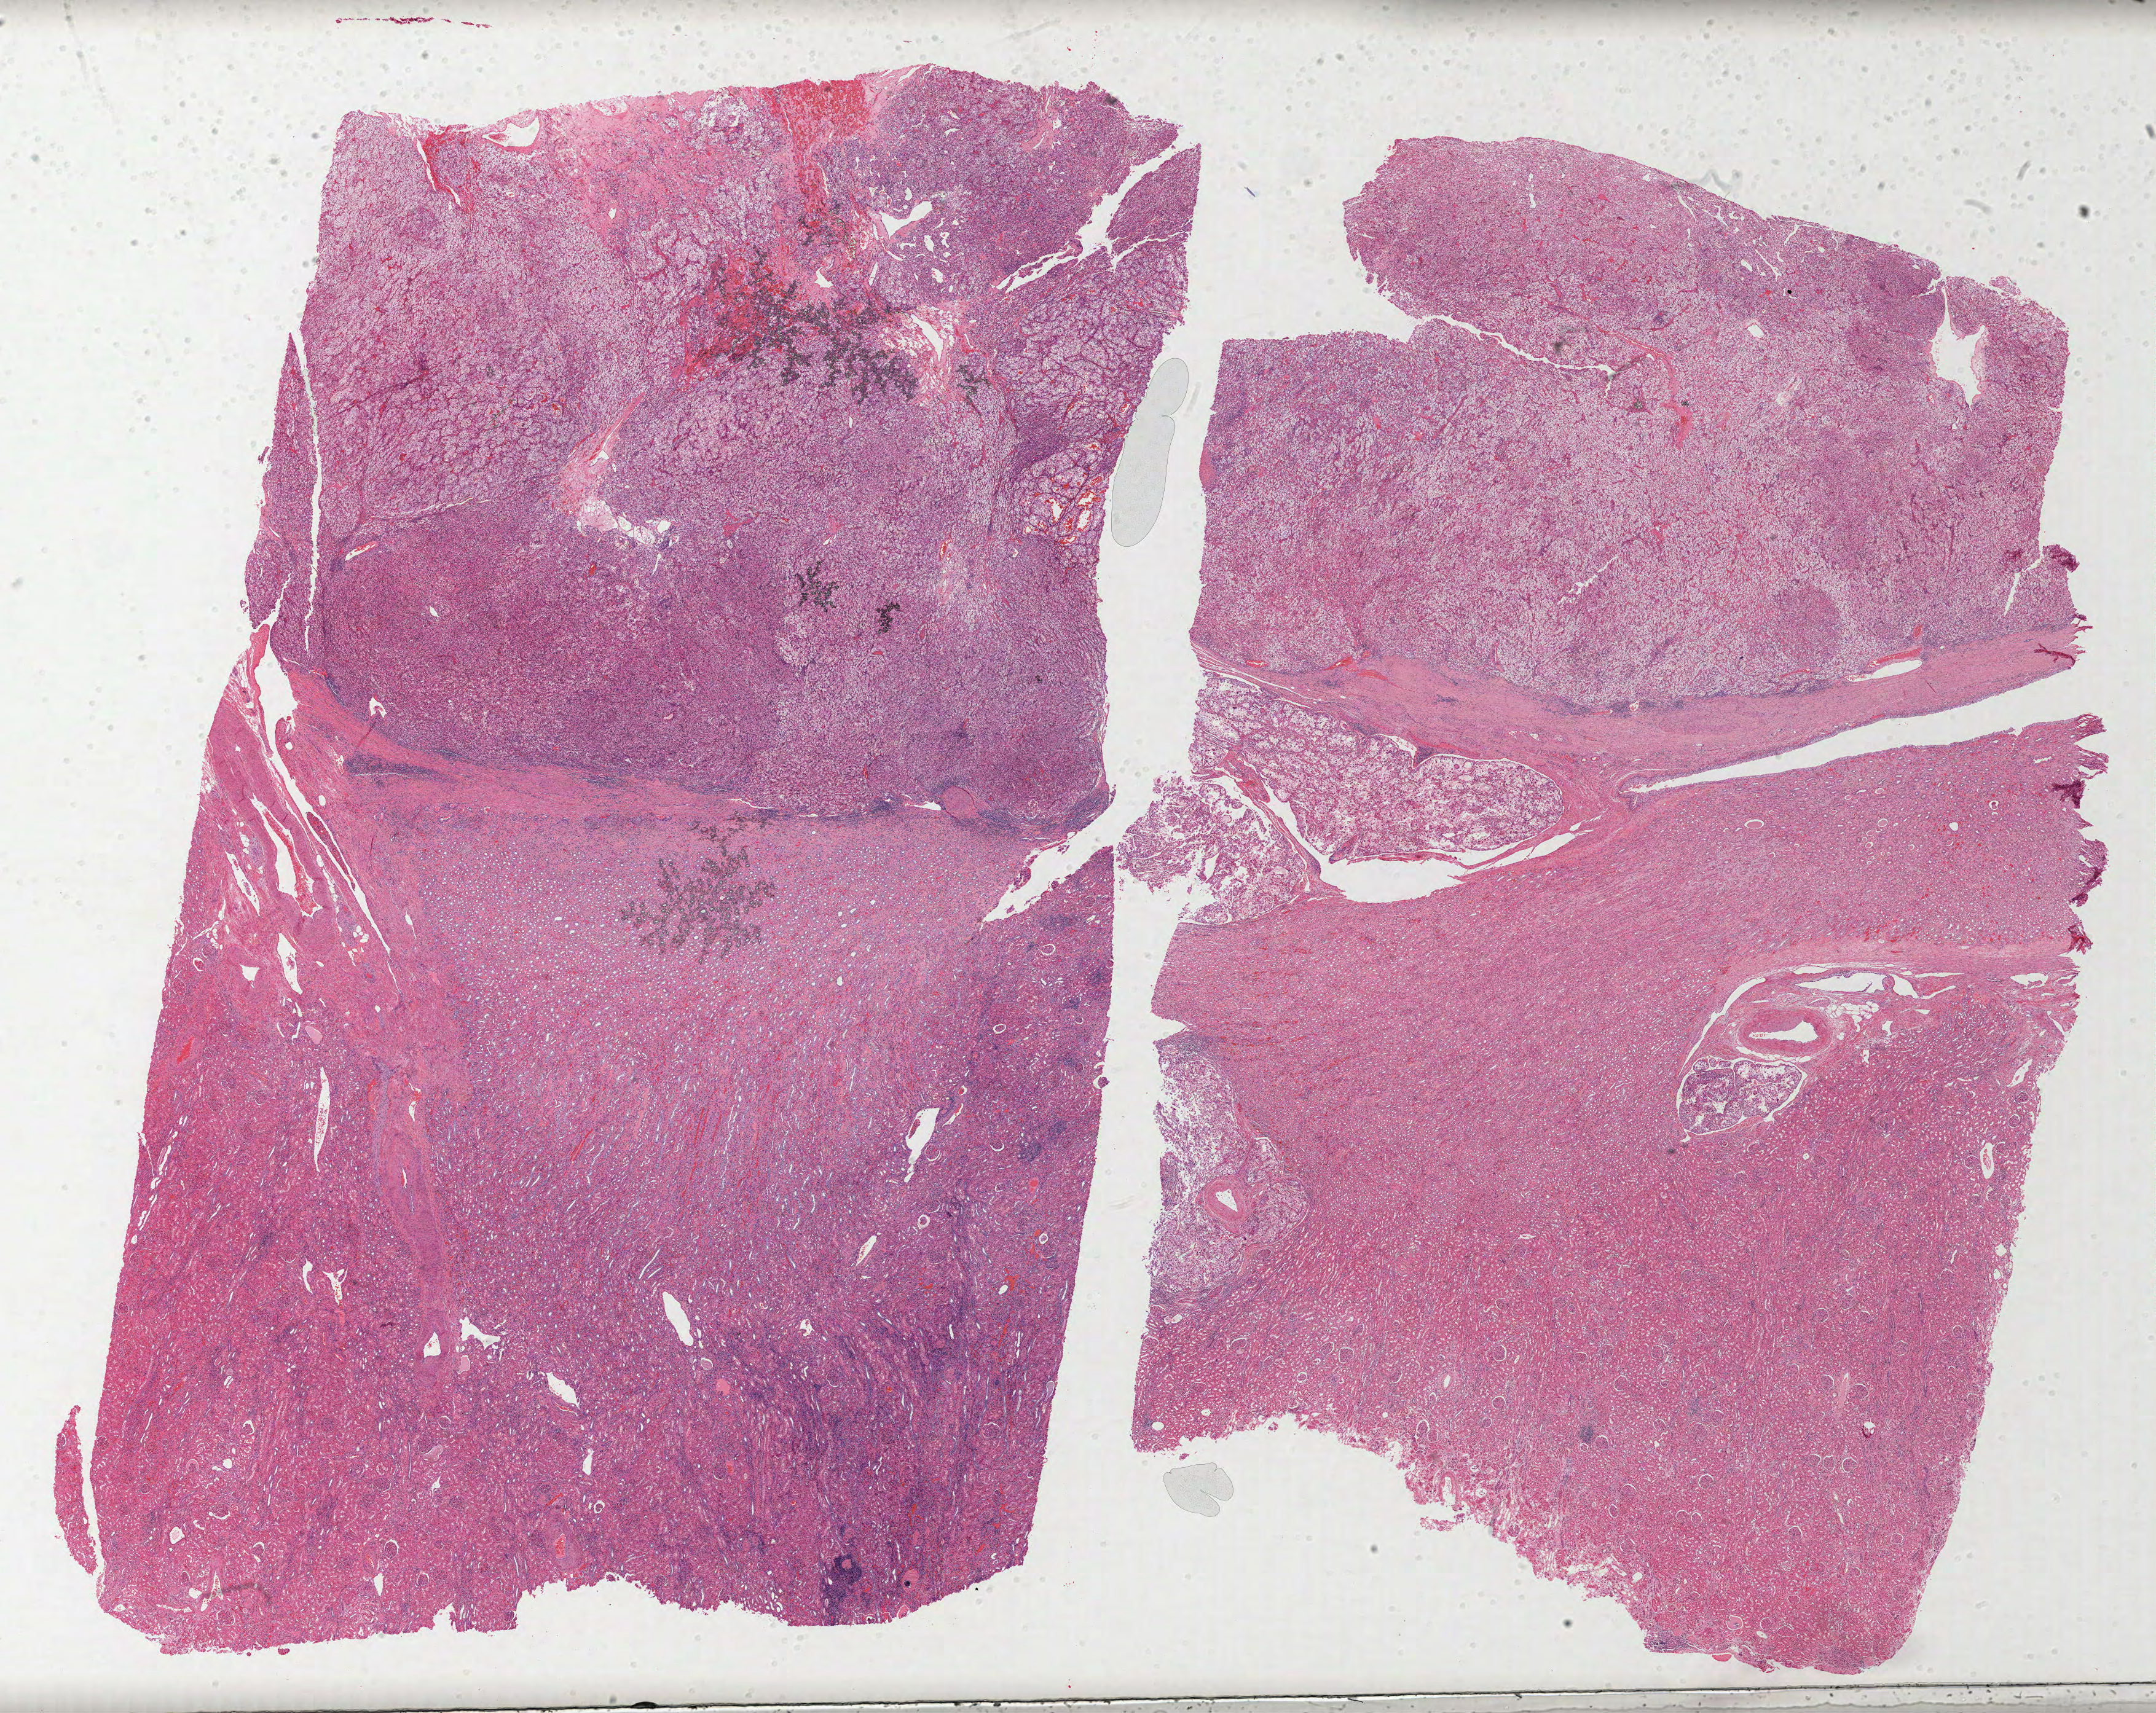
Digitized H&E-stained tissue section (whole slide) — a low-resolution overview of the entire scanned area, about 28.3 x 22.5 mm. Formalin-fixed paraffin-embedded (FFPE) diagnostic section. Sample: primary tumour, kidney. Male patient; age at initial diagnosis 55 years. Histologic grade: G2 (moderately differentiated).
• diagnosis: Clear cell adenocarcinoma, NOS
• laterality: right
• AJCC pathologic stage: IV (6th edition)
• TNM: T3b NX M1